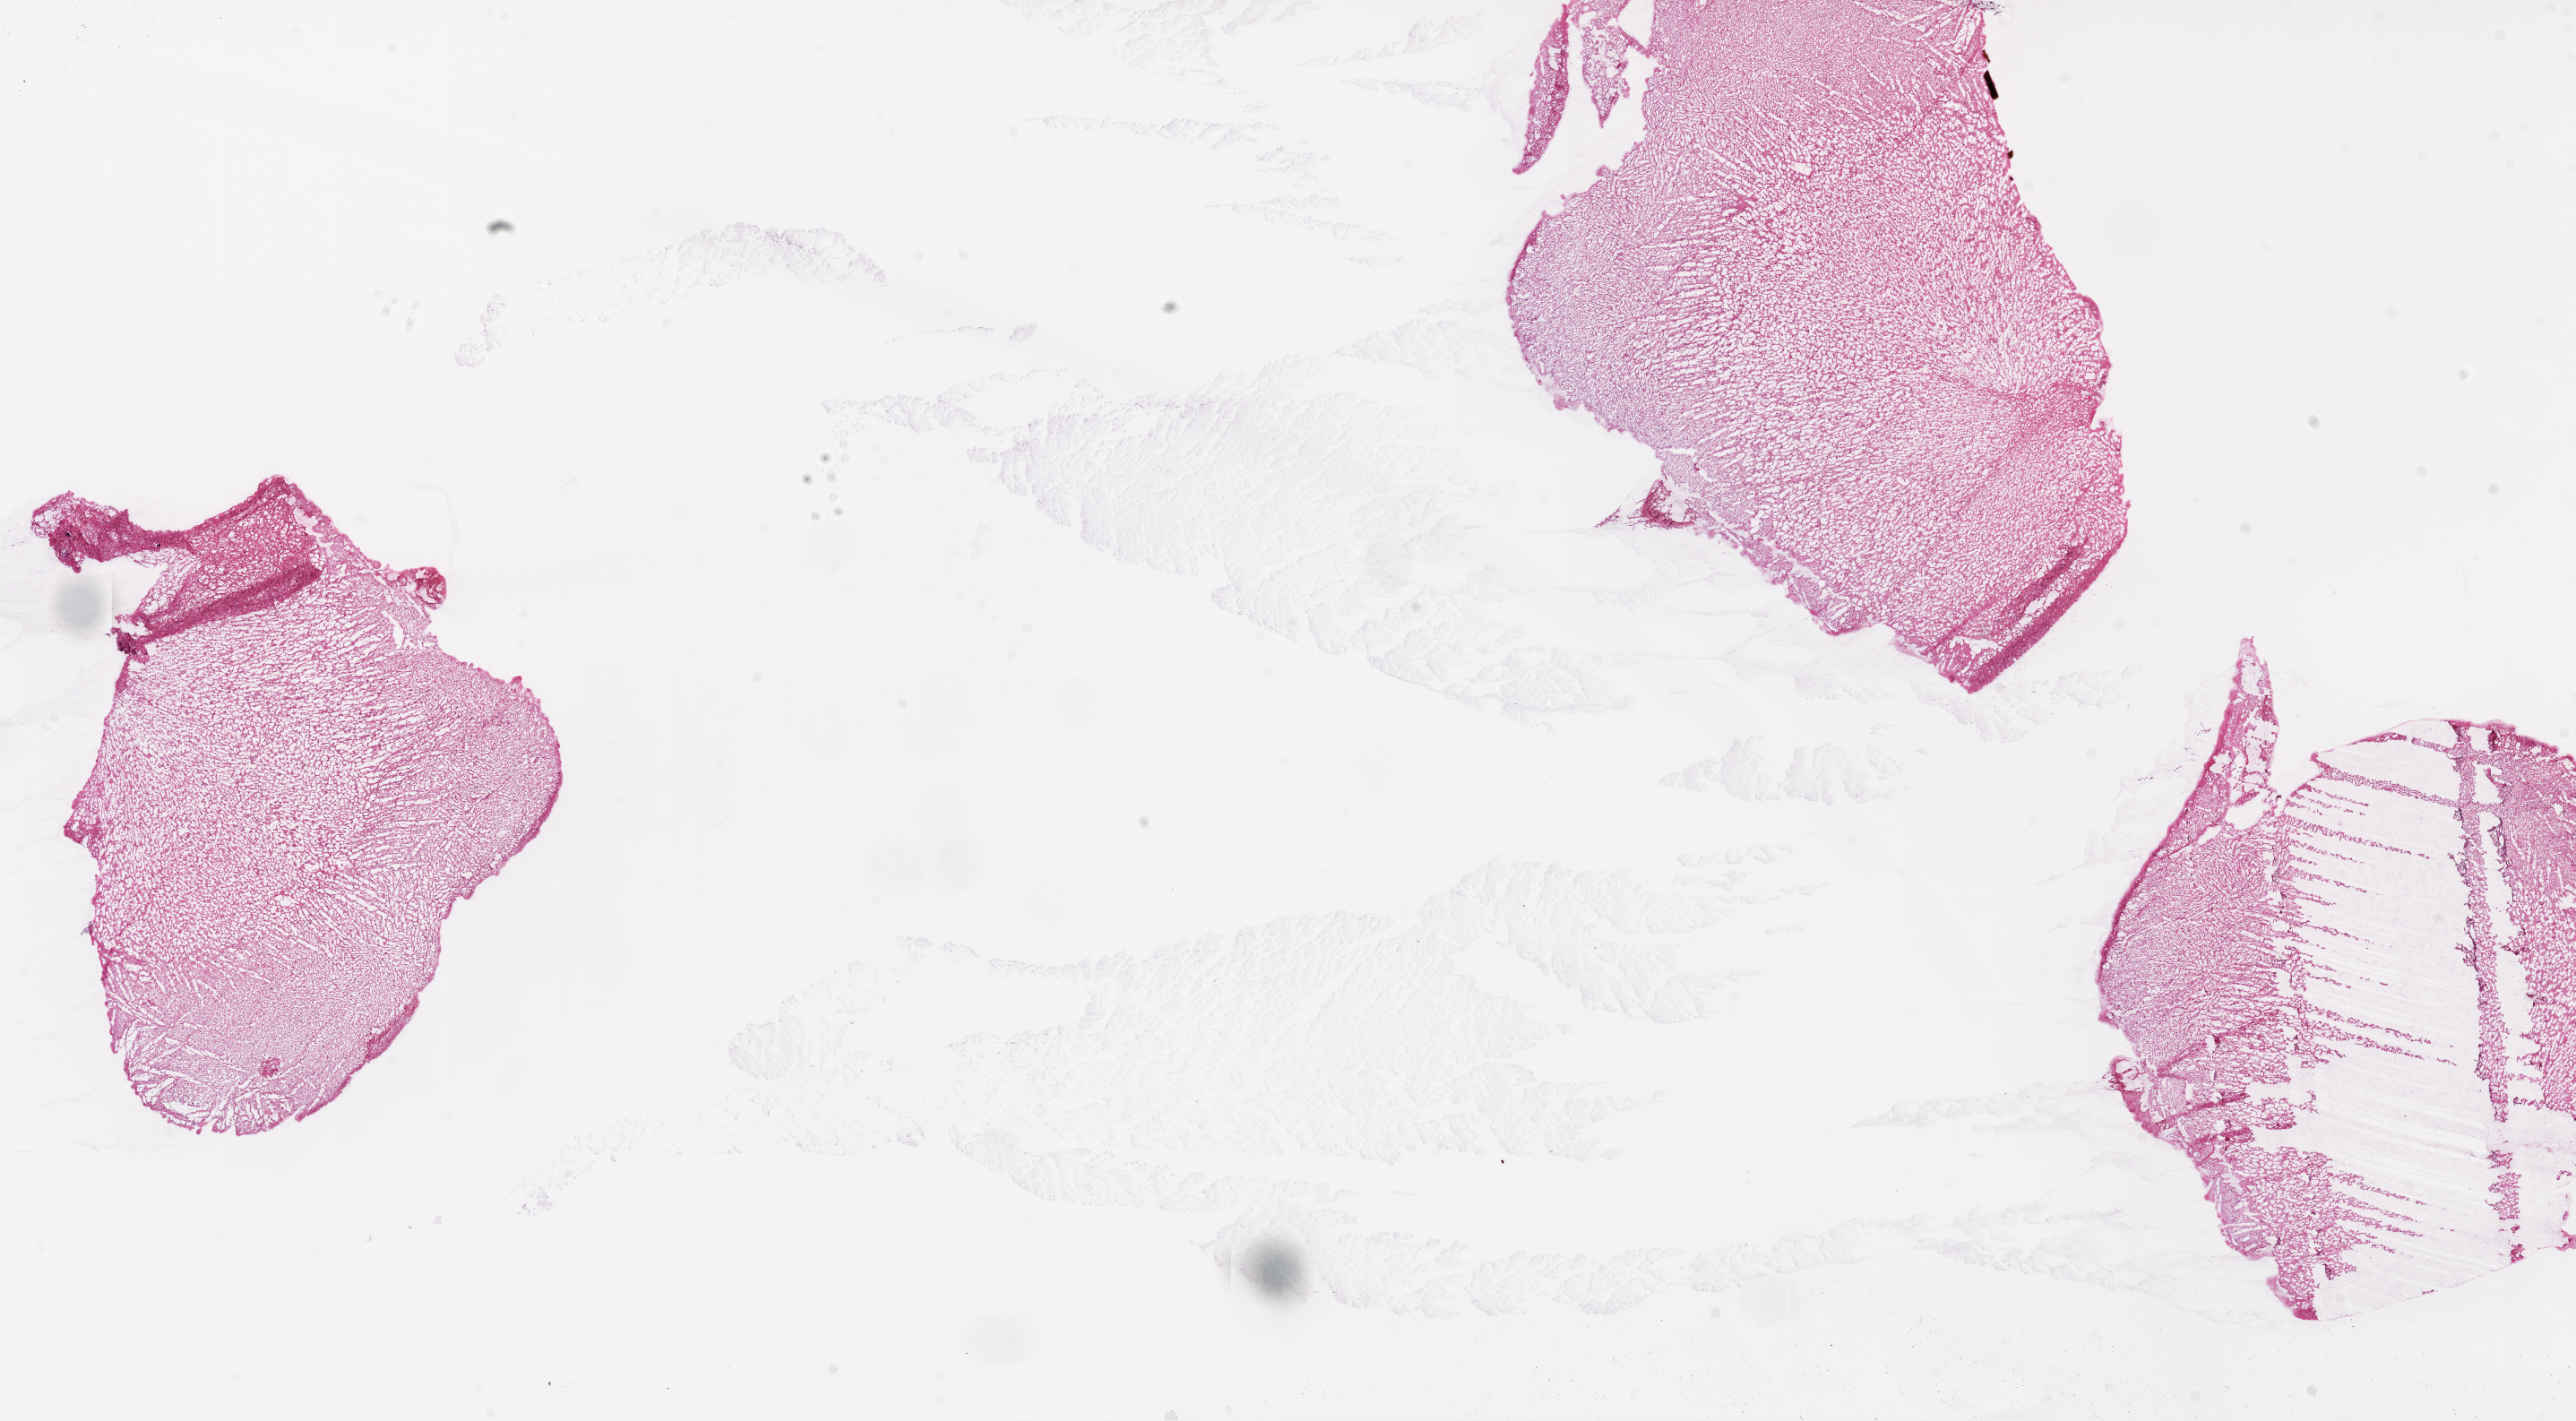
H&E whole-slide image — a low-resolution overview of the entire scanned area, about 23.1 x 12.7 mm (acquisition: 20x scan). Frozen section. Brain, primary tumour sample. Patient: male, age at initial diagnosis 30 years.
Diagnosis: Mixed glioma (cerebrum).